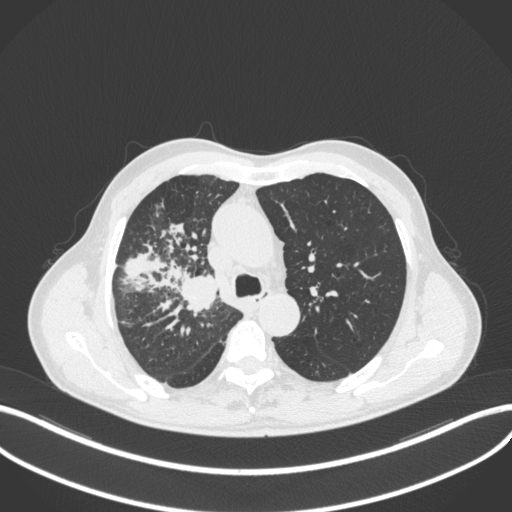
Chest CT, one axial slice. Position 335 of 490 along the scan axis. Reconstruction kernel B31f. 120 kVp. Lung window (W 1500 / L -600 HU). 1 mm slice thickness. 512 × 512 image matrix, field of view 400 × 400 mm. Patient: male, 69 years. From the clinical record (not read from this slice): clinical TNM (as recorded): T2a N0 M0.
Structures marked on this image (bounding box drawn by a radiologist):
- lung tumour (recorded histology: adenocarcinoma): bounding box [x1, y1, x2, y2] px = [178, 270, 220, 317]